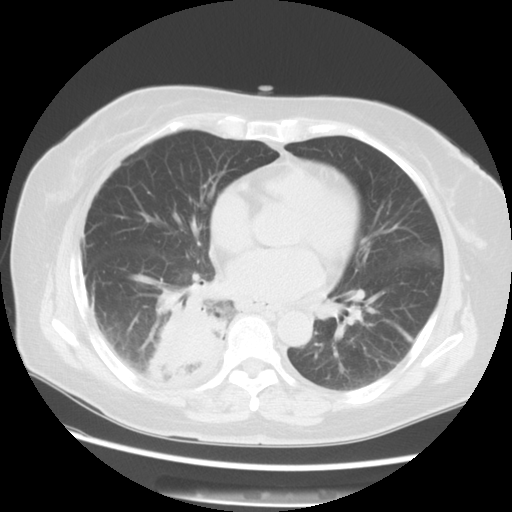
Chest CT, one axial slice. Slice 28 of 57 in the series (ordered by position). 120 kVp. Lung window (W 1500 / L -600 HU). 5 mm slice thickness. 512 × 512 image matrix, field of view 350 × 350 mm. Patient: female, 69 years. Case-level facts recorded for this patient, not image findings: clinical TNM (as recorded): T2 N1 M1a.
Outlined on this slice (bounding box drawn by a radiologist):
- lung tumour (recorded histology: adenocarcinoma): bounding box (x1, y1, x2, y2) in pixels: (143, 298, 227, 392)